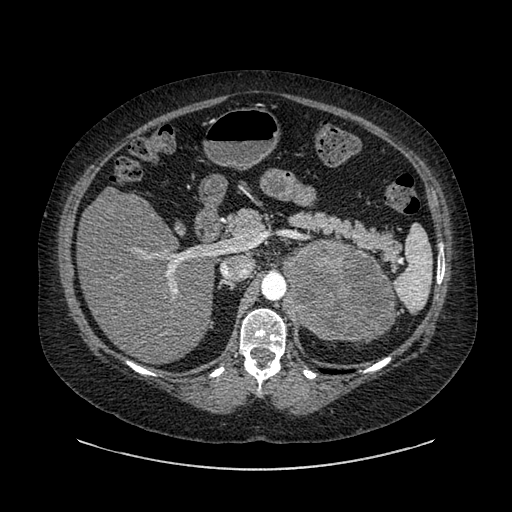
Contrast-enhanced abdominal CT, one axial slice. Slice 572 of 769 in the series (ordered by position). 120 kVp. Intravenous contrast given. Soft-tissue window (W 400 / L 40 HU). 512 × 512 image matrix, field of view 460 × 460 mm. Female patient, age 61 years. From the clinical record (not read from this slice): diagnosis: adrenocortical carcinoma; tumour side: left adrenal; tumour size at pathology: 13 cm; Ki-67 index: 79 %; stage (as recorded): 2.
Structures marked on this image (semi-automatically segmented with operator editing):
- mass: bounding box [x1, y1, x2, y2] px = [282, 240, 395, 342]